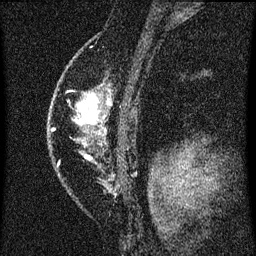
Breast MRI (dynamic contrast-enhanced), one sagittal slice; slice 48 of 60 in the series (ordered by position); dynamic contrast-enhanced series, image 2 of 3 at this slice position (ordered by acquisition); 1.5 T; TE 4.2 ms, TR 8 ms; 2 mm slice thickness; 256 × 256 image matrix. Patient: female, 46 years.
Outlined on this slice (semi-automatic segmentation, software-assisted and operator-edited):
- analysis volume of interest (the breast-tissue region the enhancement analysis was run in; not a lesion): bounding box (x1, y1, x2, y2) in pixels: (56, 72, 111, 187)
- tumour enhancement mask (voxels above the 70 % enhancement threshold inside the analysis volume of interest): (78, 94, 98, 125)